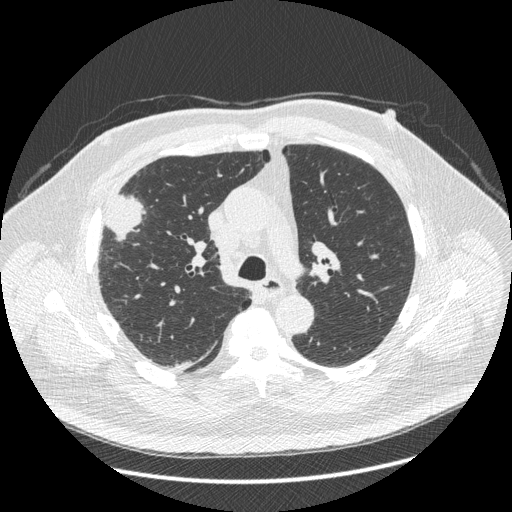
Chest CT (low-dose screening protocol), one axial image; third screening round (two years after baseline); lung window (W 1500 / L -600 HU); 1.25 mm slice thickness; standard (soft-tissue) reconstruction kernel (STANDARD); 120 kVp; slice 143 of 426 in the series. Male, age 66 years at enrolment. Current smoker at enrolment.
Expert-annotated lung lesion, box from (x=86, y=187) to (x=145, y=266) px. Screening reader's record for this exam (one nodule recorded; not confirmed to be the boxed lesion): non-calcified nodule or mass ≥4 mm, right upper lobe, 48 × 25 mm, spiculated (stellate) margins, soft tissue attenuation, pre-existing on the prior screen: no. Lung cancer was diagnosed 35 days after this screen: non-small cell carcinoma, right upper lobe, stage IV (AJCC 6th edition), 50 mm at pathology.